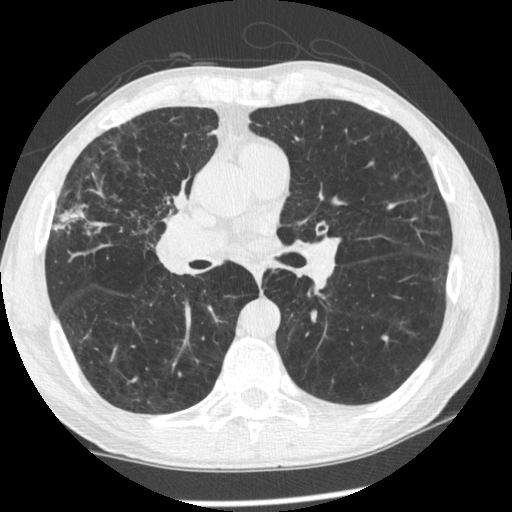
Low-dose screening chest CT, one axial slice. Position 125 of 261 along the scan axis. Lung window (W 1500 / L -600 HU). 1.25 mm slice thickness. 512 × 512 image matrix, field of view 340 × 340 mm.
Outlined on this slice (expert manual segmentation):
- lesion 1 (tumor, upper lobe of right lung): box from (x=173, y=180) to (x=188, y=210) px